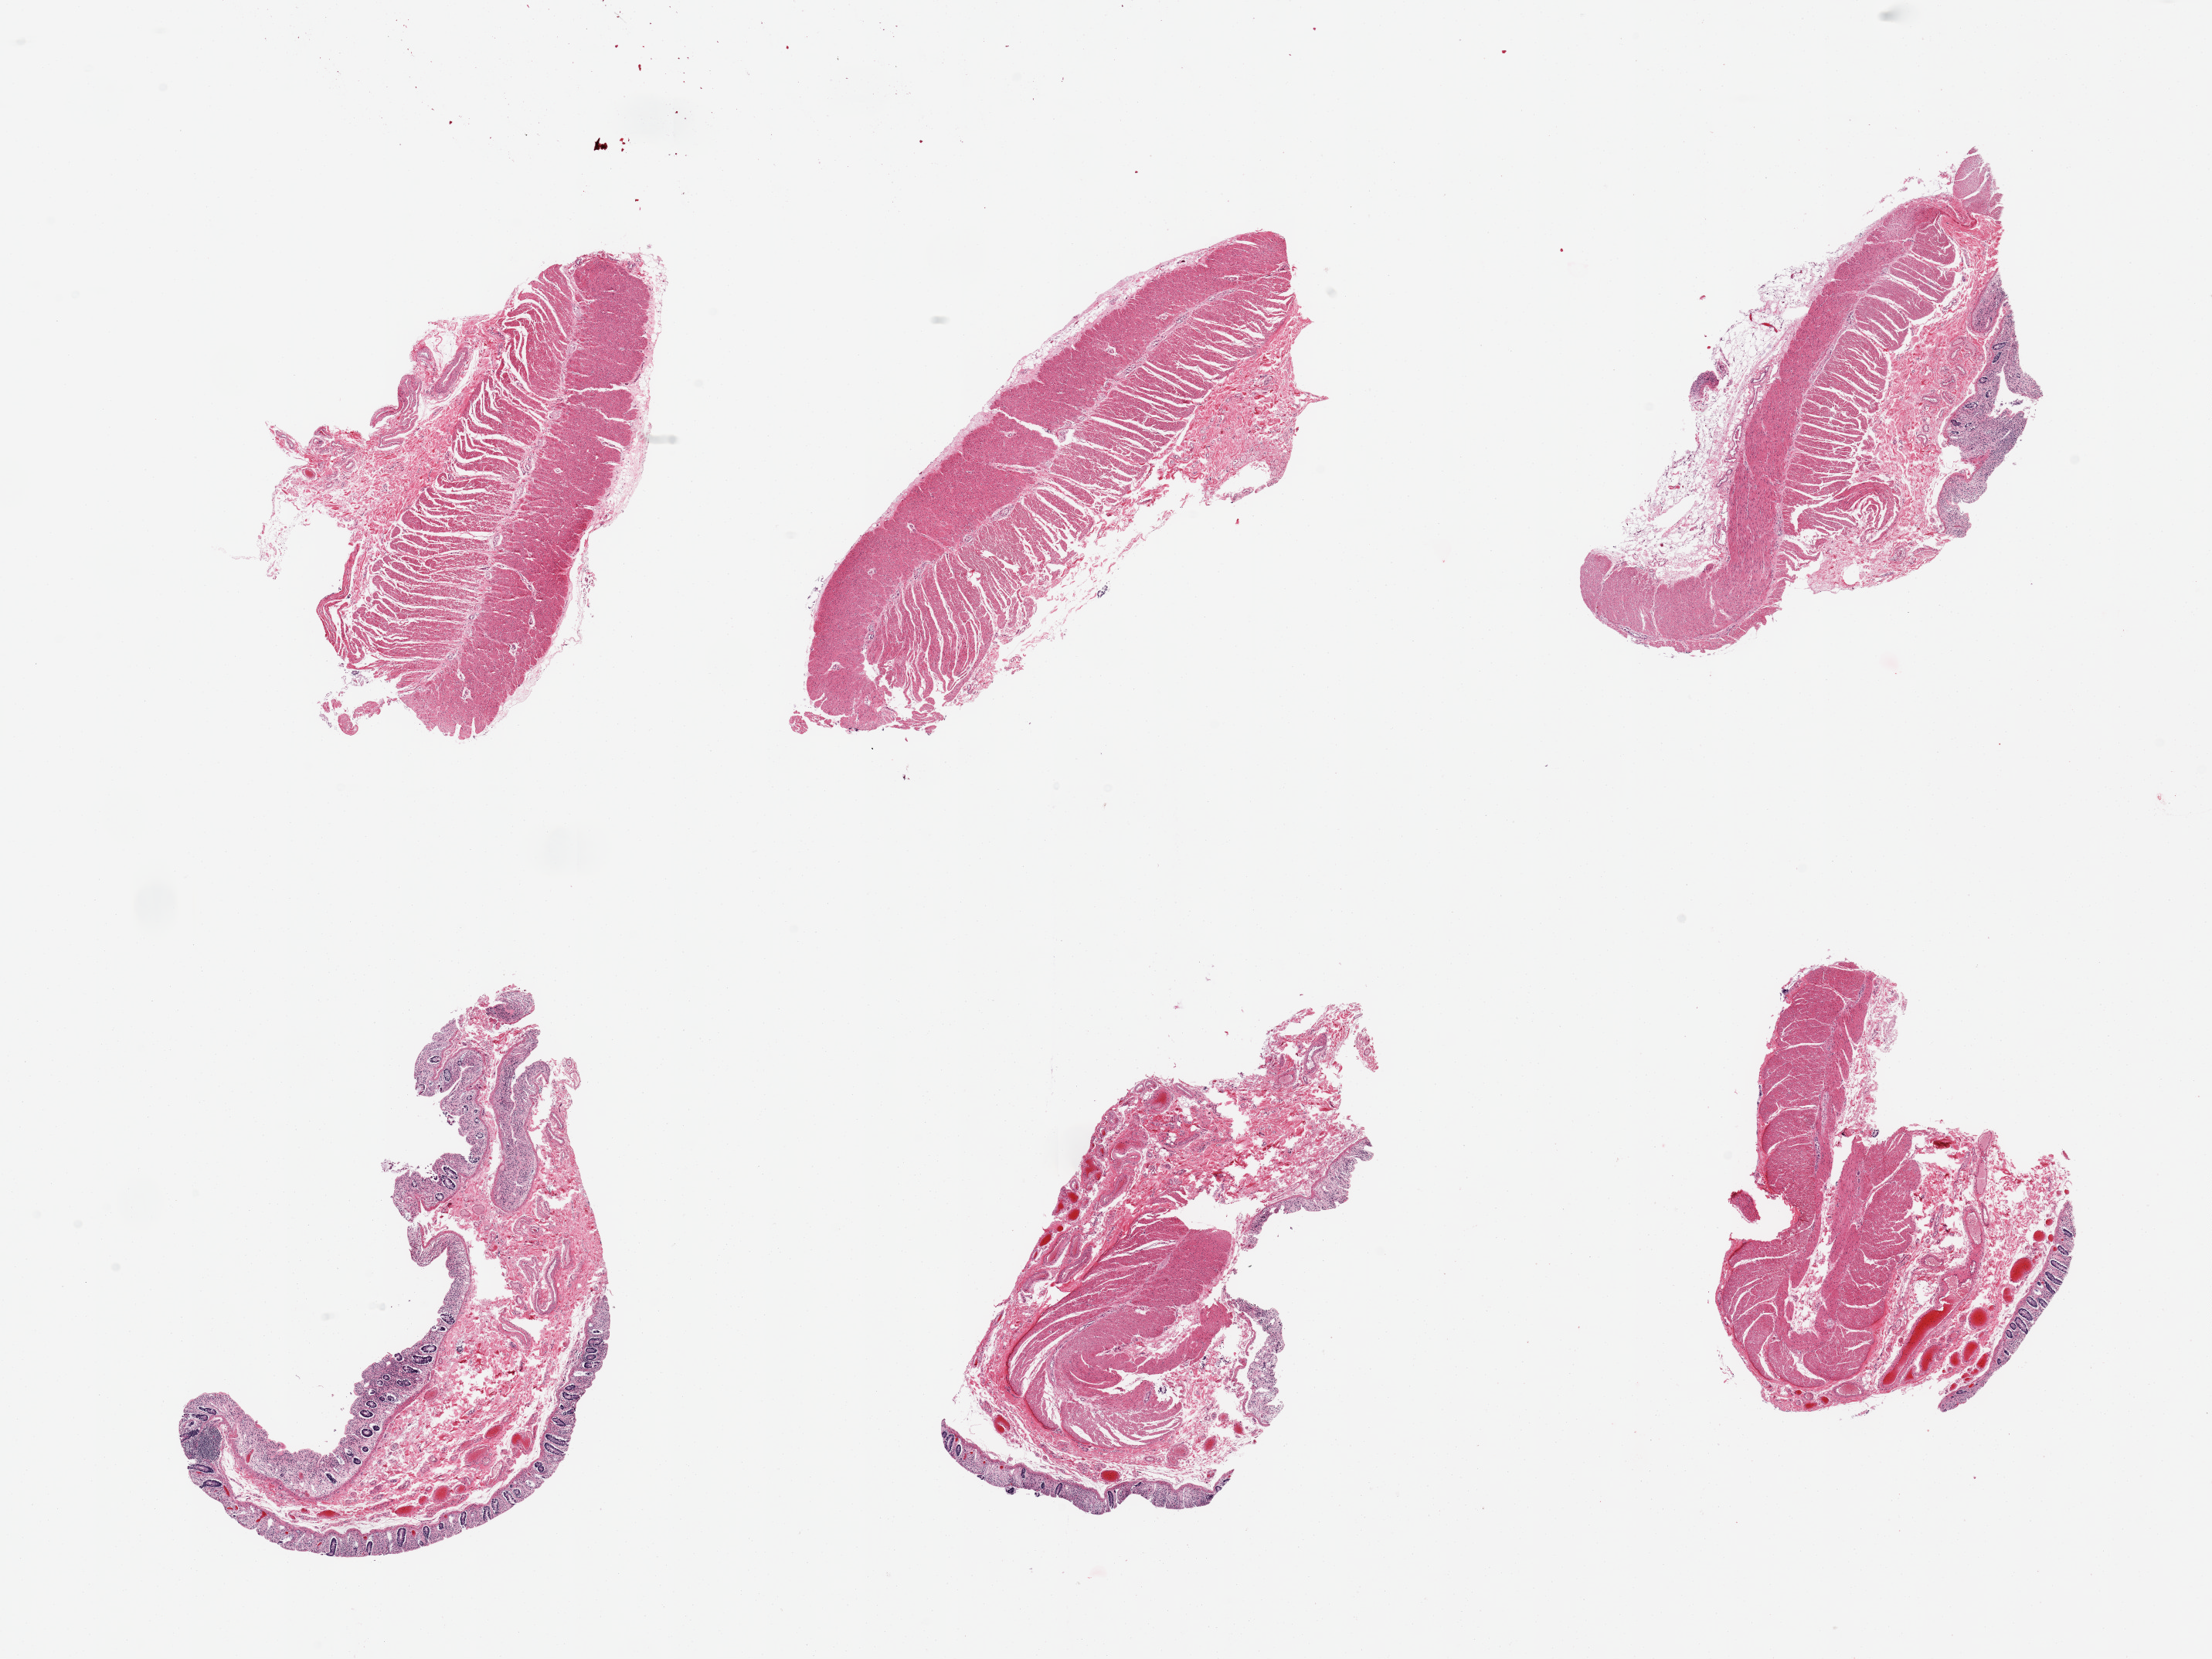
Digitized hematoxylin and eosin (H&E)-stained section, low-resolution overview of the scanned area, about 22.6 x 17.0 mm (from a 20x scan); PAXgene-fixed, paraffin-embedded tissue; sampled site (target tissue): transverse colon; donor tissue sample. Donor sex: female.
Review note (as recorded): 6 pieces, target mucosa up to ~0.3mm, advanced autolysis, partially sloughed.